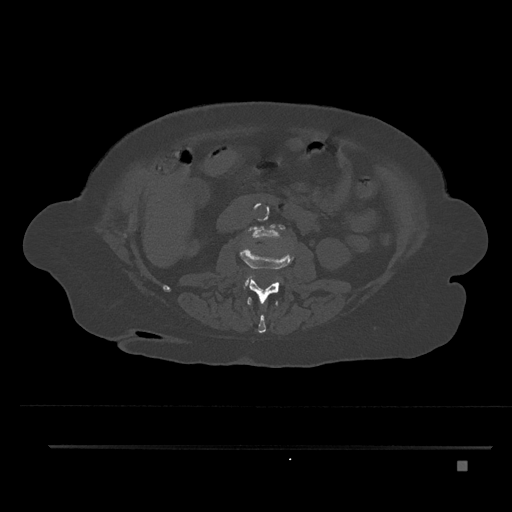
CT including the spine, one axial slice; slice 169 of 797 in the series (ordered by position); bone window (W 1800 / L 400 HU); 0.5 mm slice thickness; 512 × 512 image matrix, field of view 437 × 437 mm. Patient: female, 76 years. Case-level facts recorded for this patient, not image findings: primary cancer: lung; vertebrae with lytic lesions (as recorded): T11, L3.
Annotated regions visible in this slice (semi-automatic segmentation, software-assisted and operator-edited):
- L1 vertebra: bounding box [x1, y1, x2, y2] px = [247, 297, 278, 333]
- L2 vertebra: [240, 248, 294, 304]
- L3 vertebra: [246, 224, 285, 285]